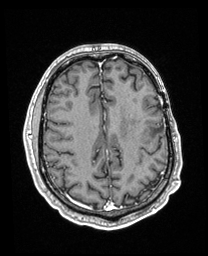
Brain MRI from a brain-tumour surgery series, one axial slice; slice 77 of 208 in the series (ordered by position); T1-weighted post-contrast; 1 mm slice thickness; 208 × 256 image matrix, field of view 211 × 260 mm. Case-level facts recorded for this patient, not image findings: histopathology: Astrocytoma; WHO grade: 3; IDH mutation: yes.
Annotated regions visible in this slice (manually delineated by an expert):
- previous resection cavity: box from (x=159, y=127) to (x=163, y=130) px